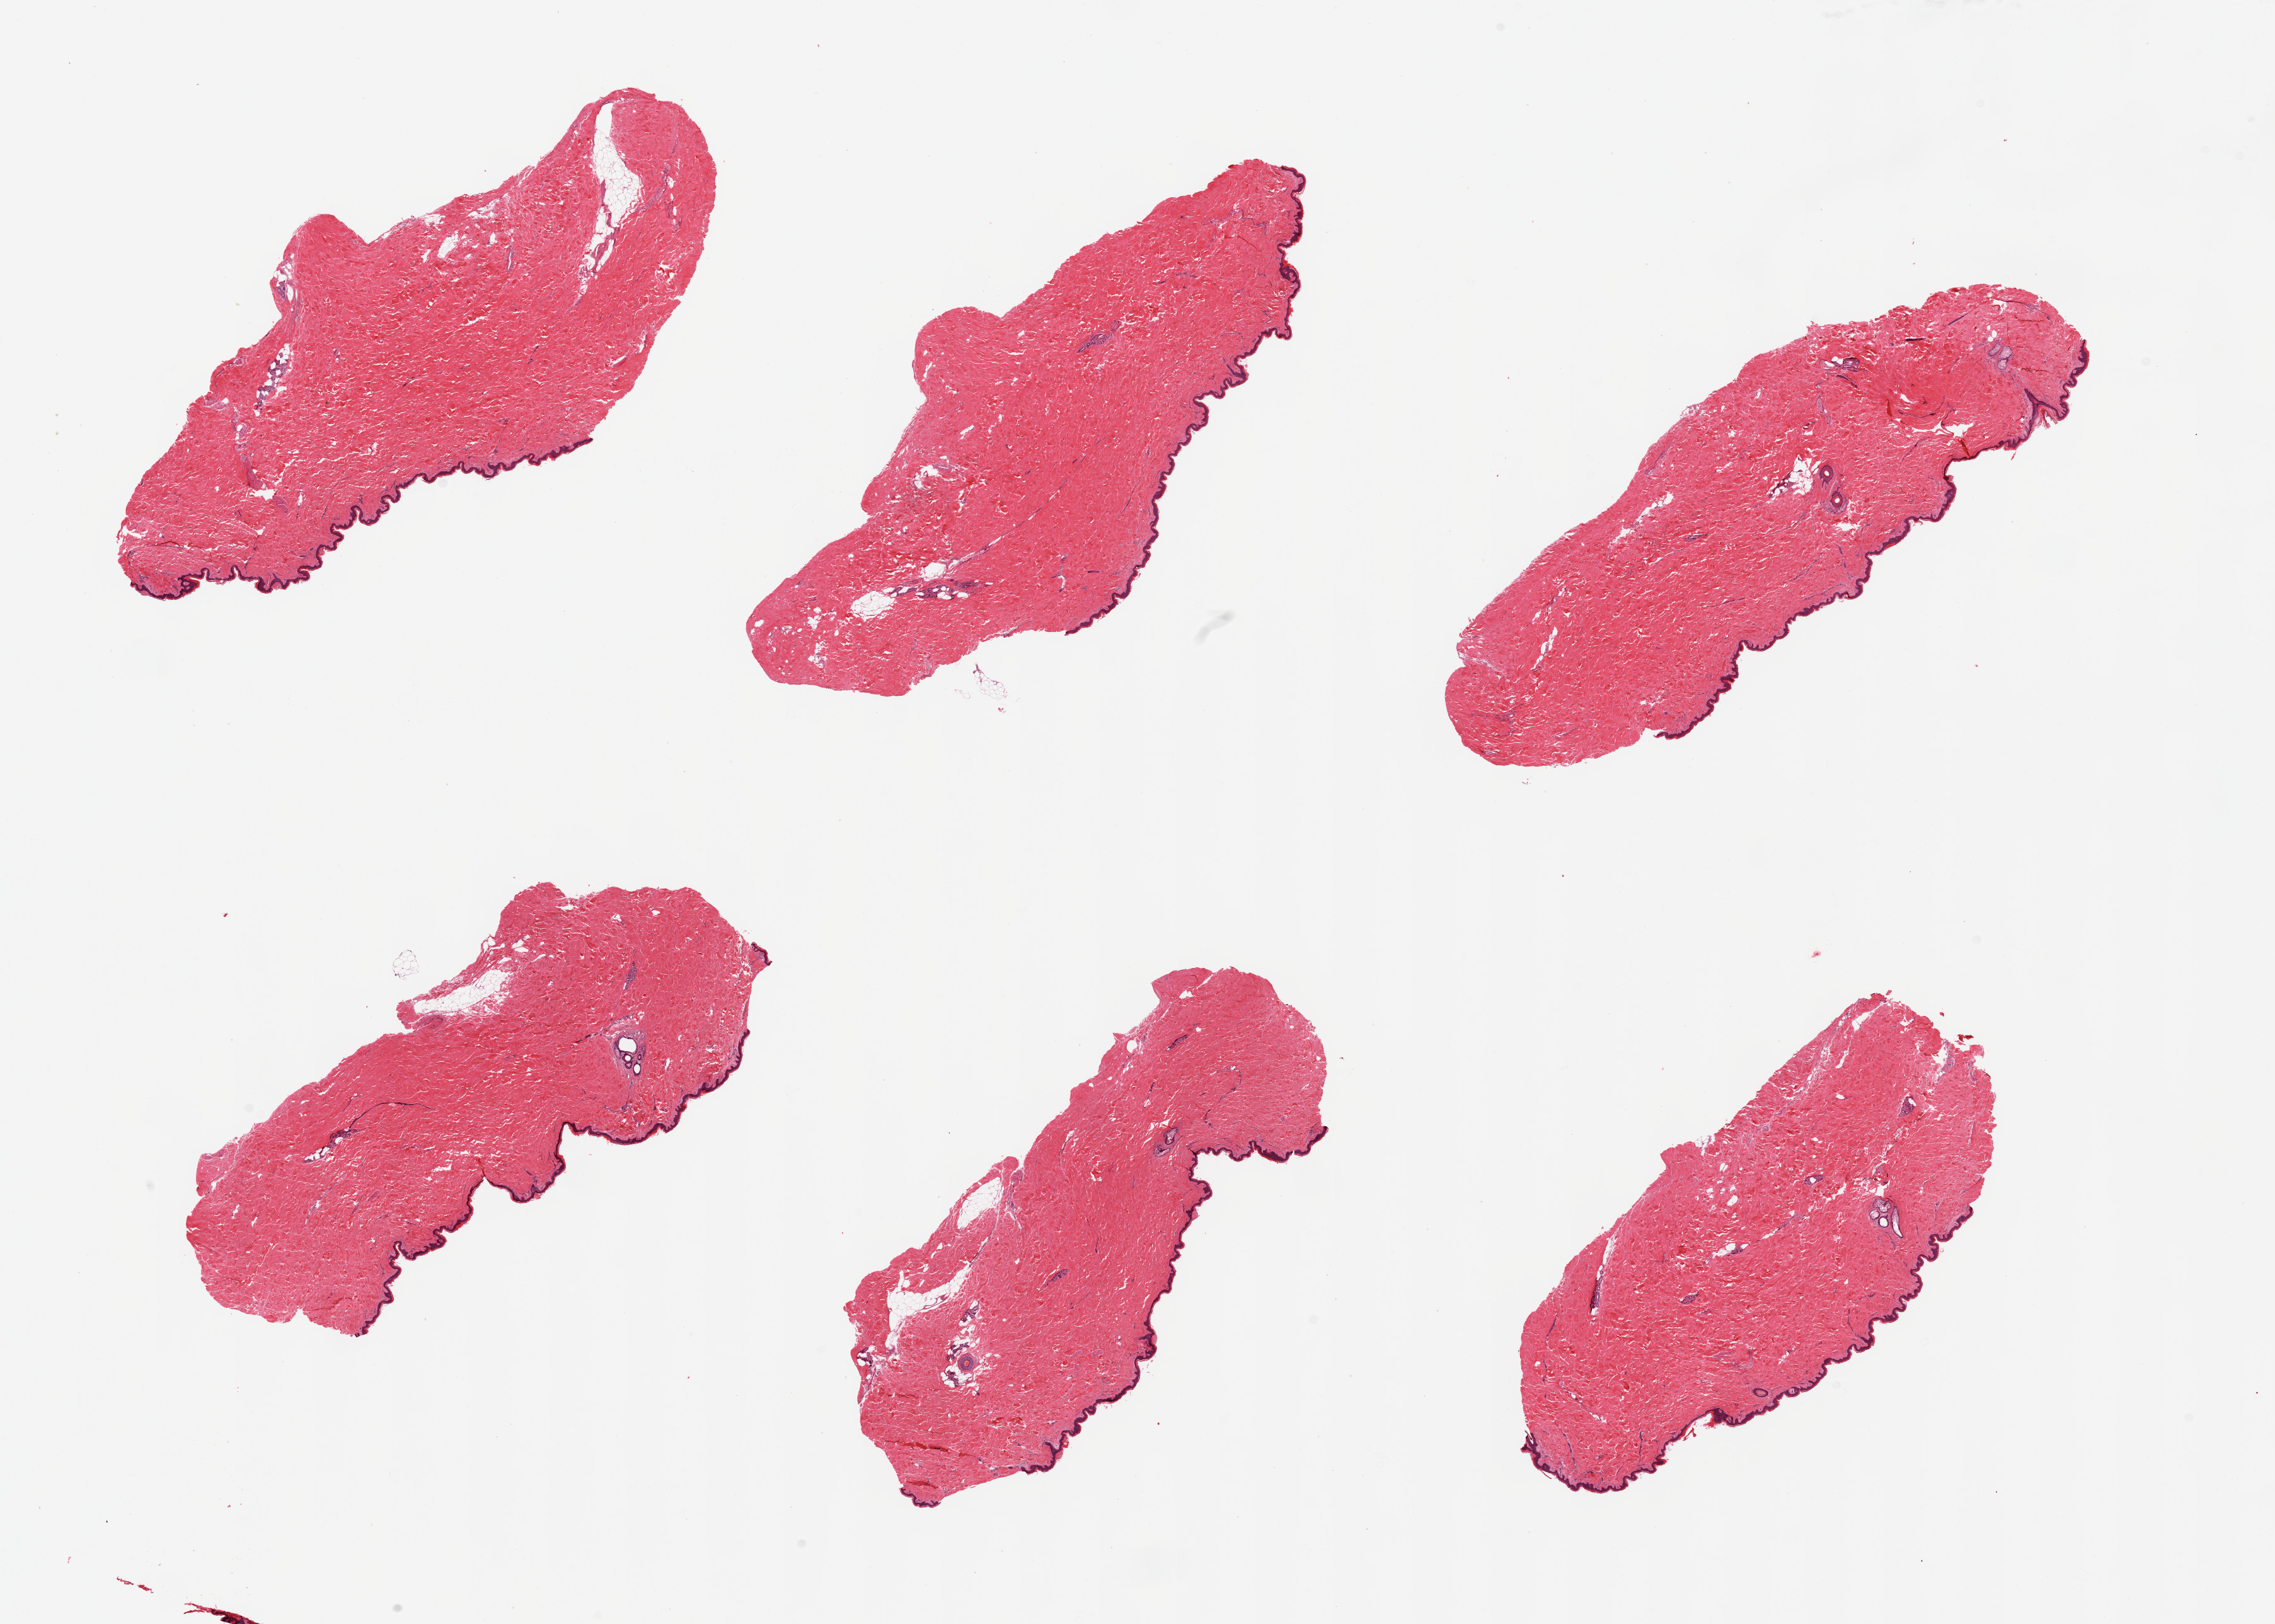
Digitized H&E-stained section, shown as a low-resolution overview of the whole scanned area (about 28.5 x 20.4 mm, slide scanned at 20x); PAXgene-fixed, paraffin-embedded tissue; section of skin of suprapubic region (target tissue); tissue donor sample.
Review note (as recorded): 6 pieces; well trimmed with scant internal fat.